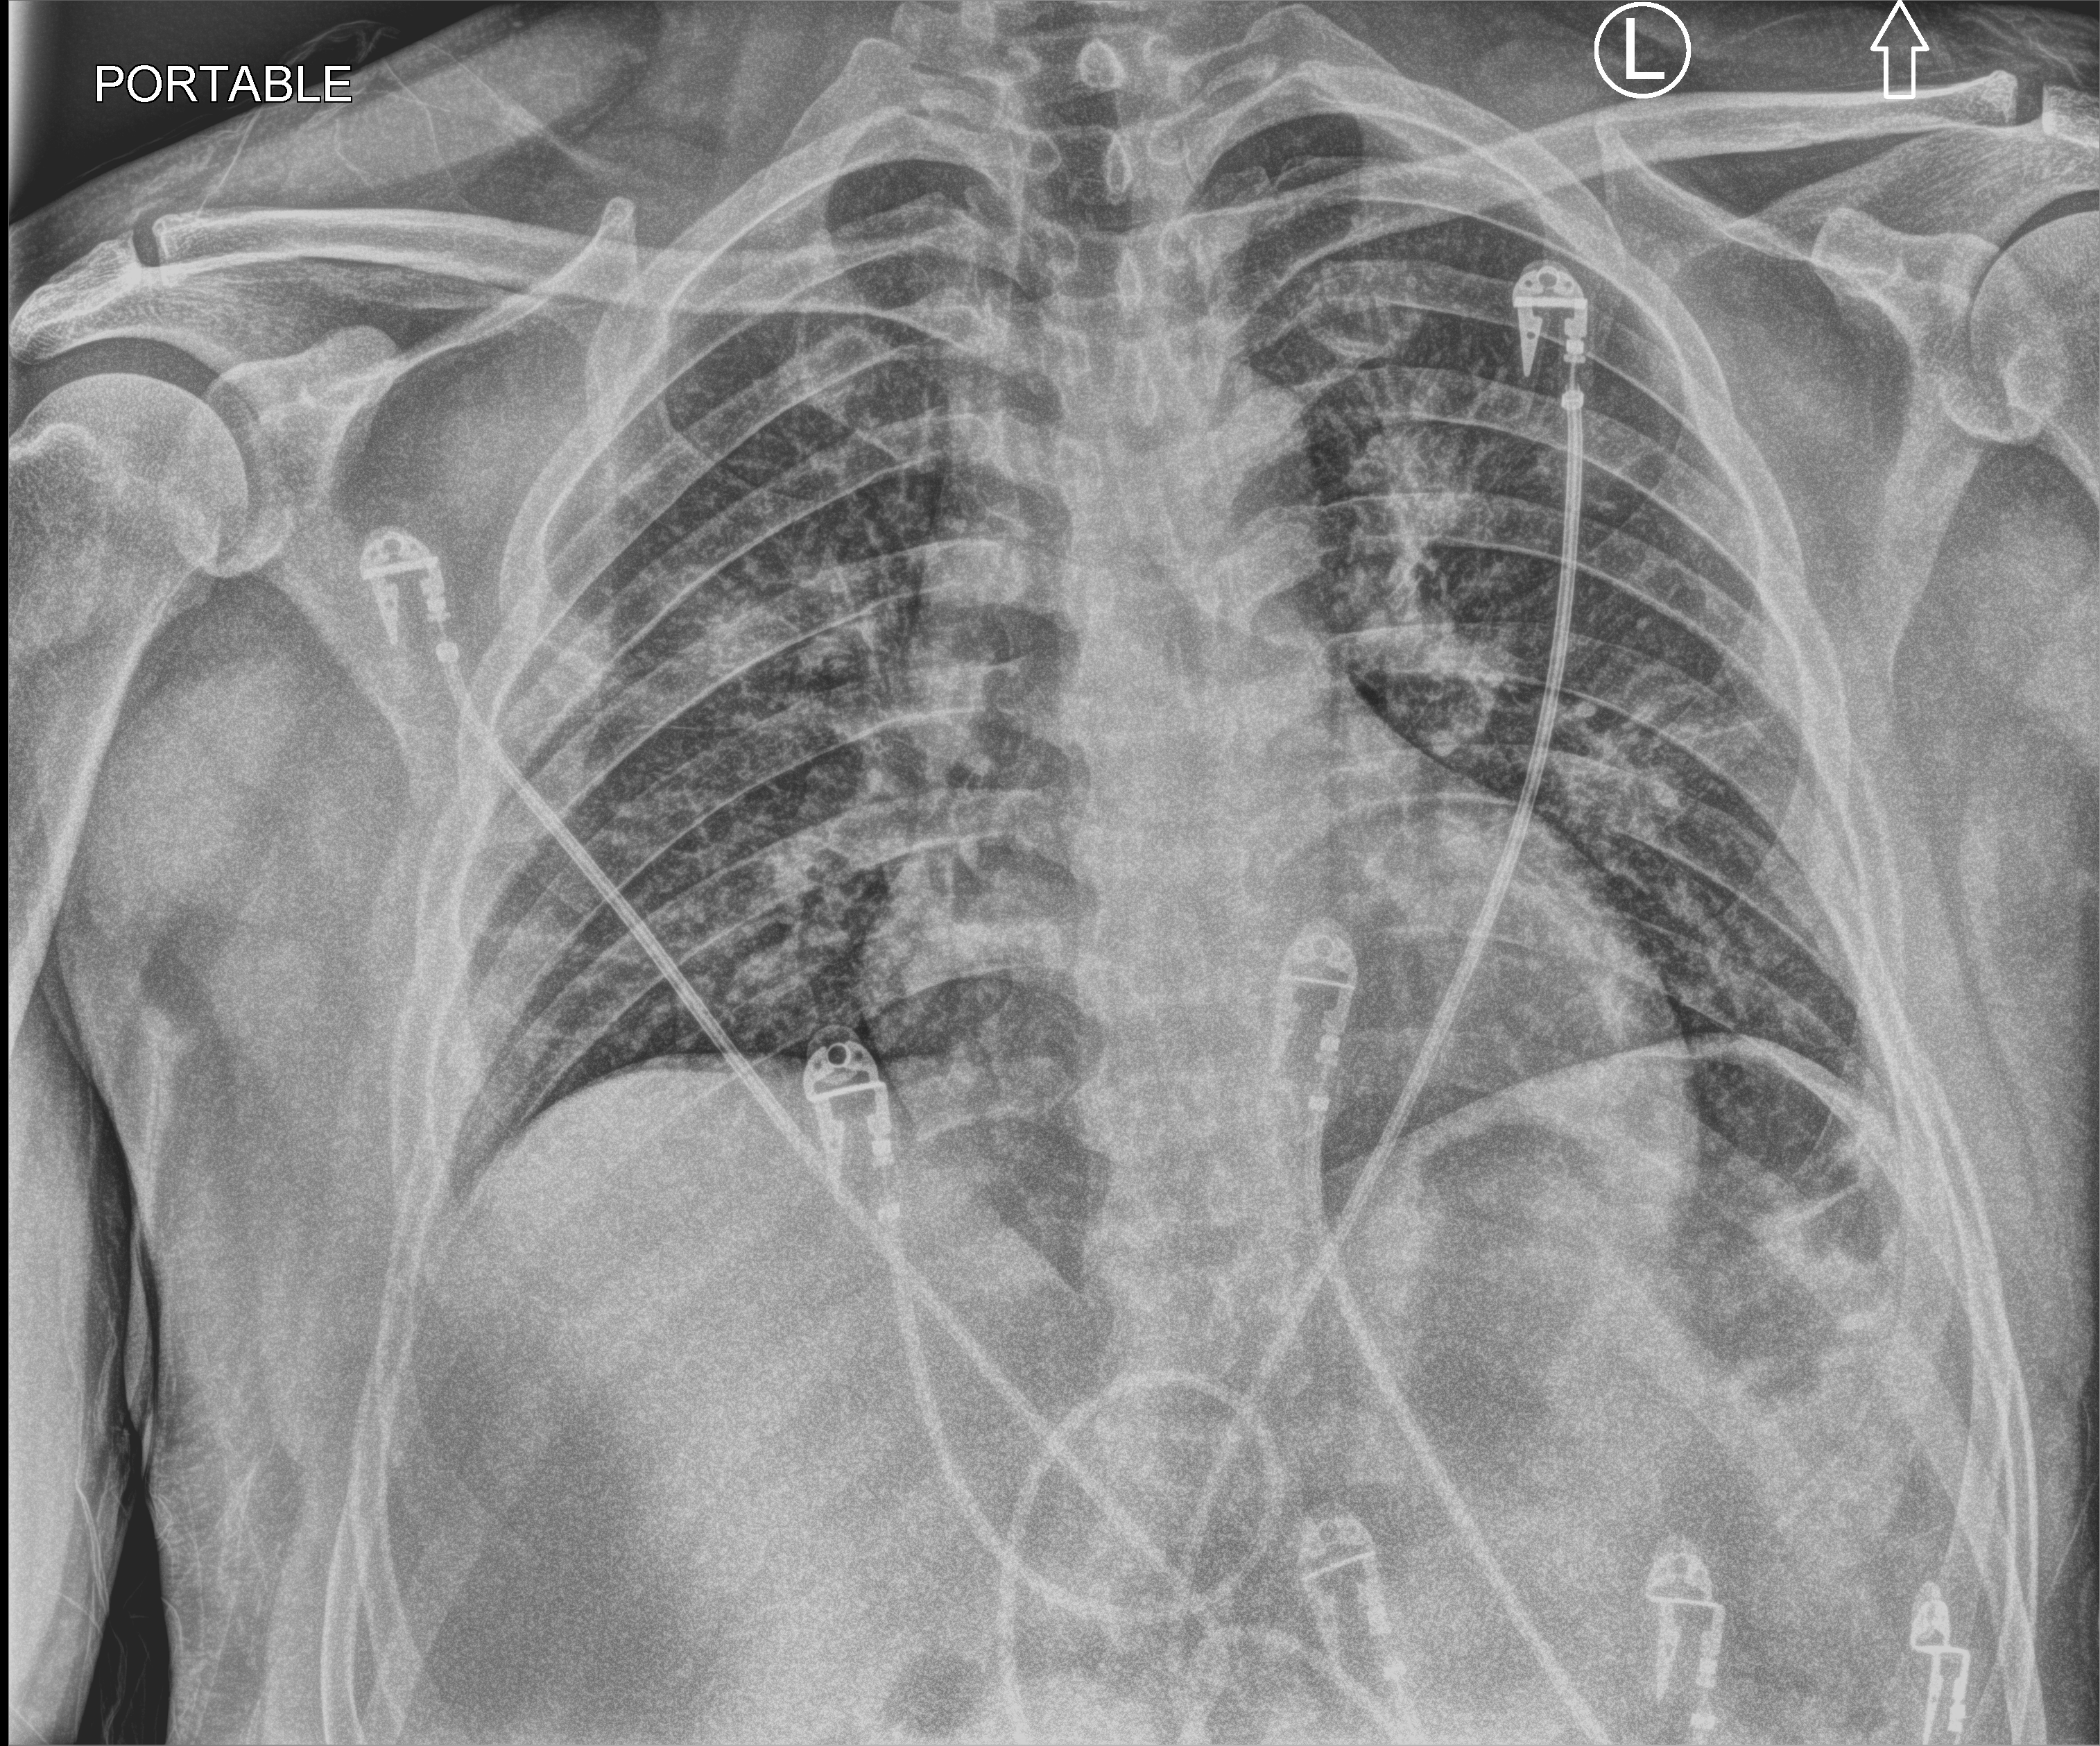
Portable chest radiograph, anteroposterior (AP) projection. Patient hospitalised with COVID-19; male, aged 18–59 years.
Hospital-stay facts (about this admission, not read from this image; timing relative to this image not recorded): mechanically ventilated during this hospital stay: no; length of hospital stay: 11 days.